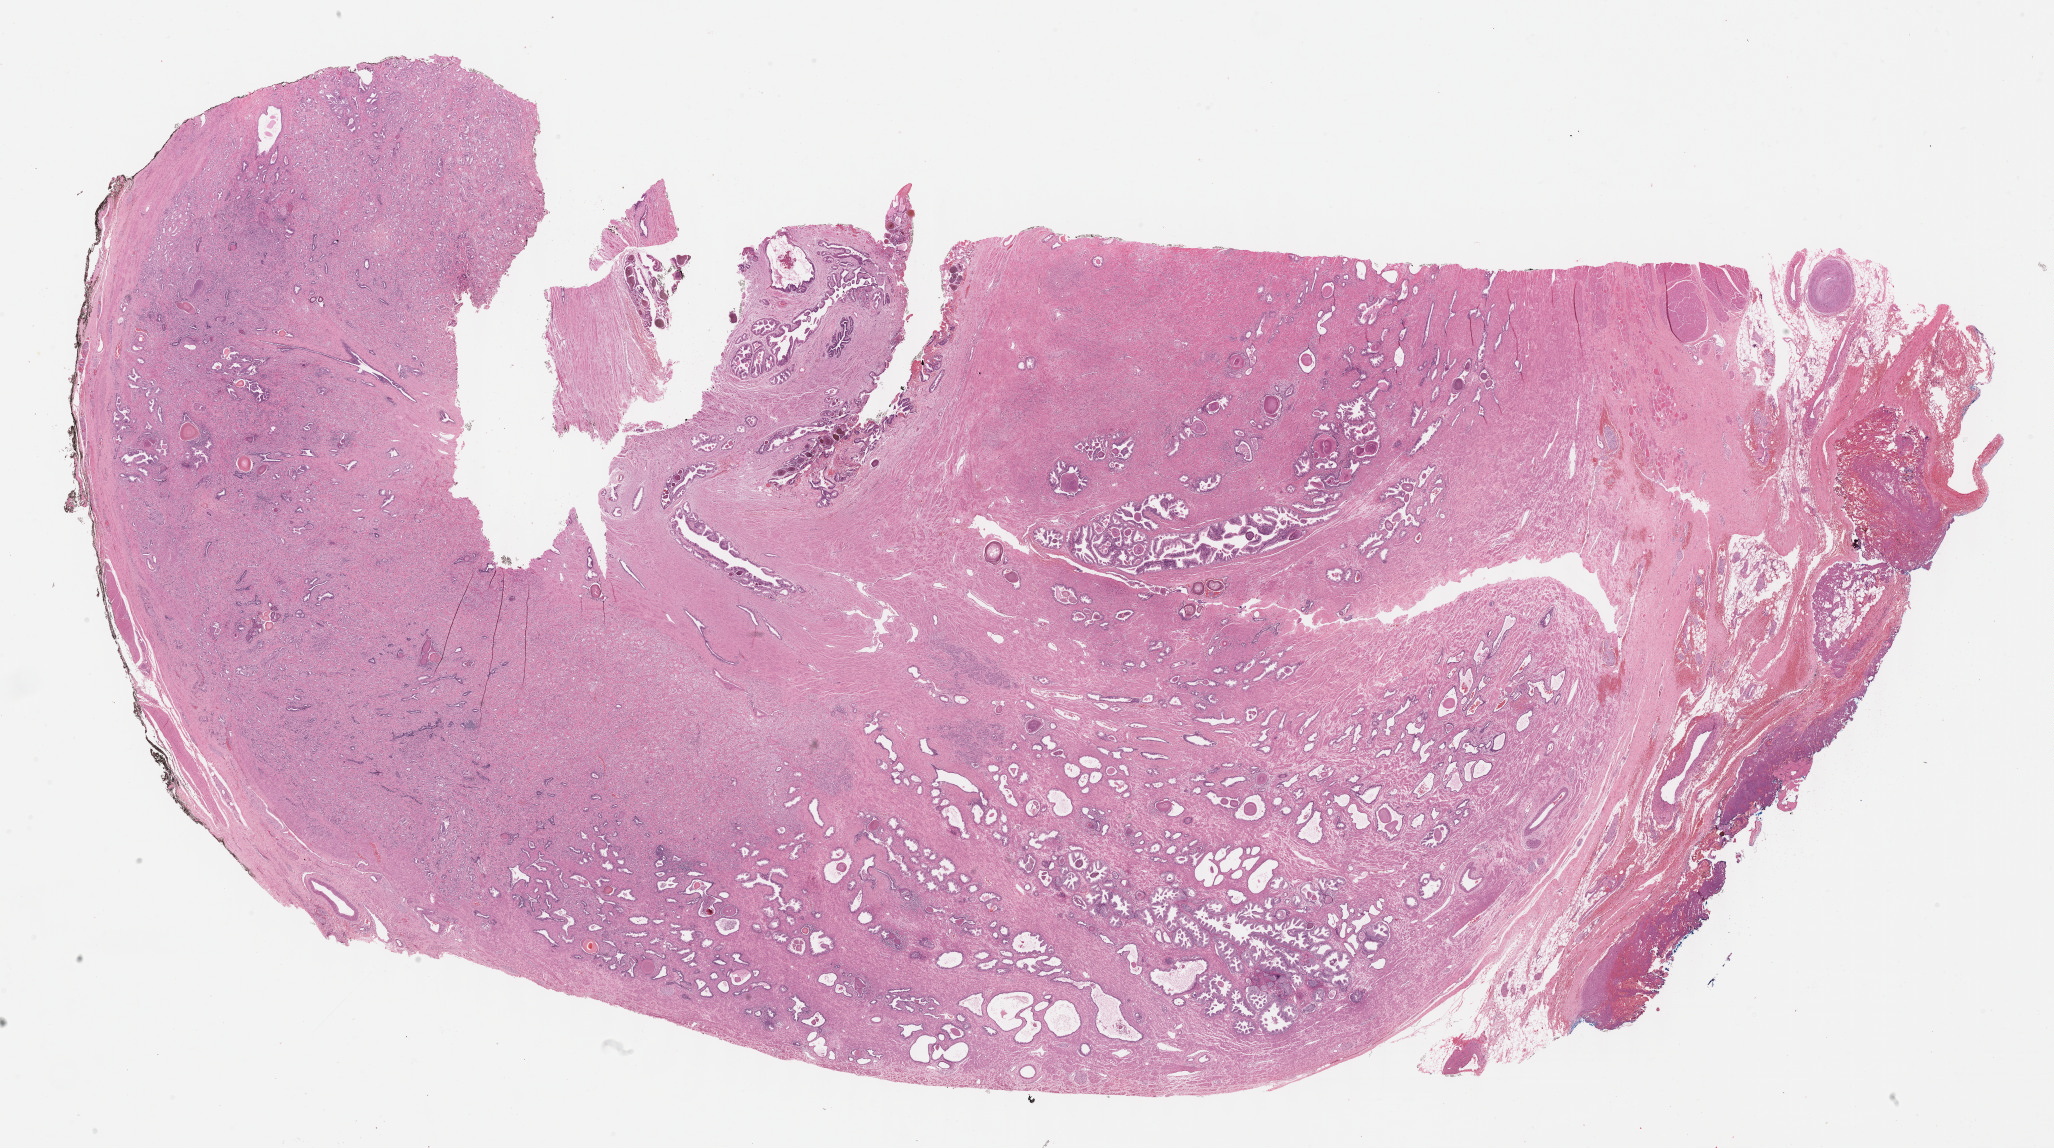
H&E whole-slide image — whole scanned area (about 33.2 x 18.6 mm, from a 40x scan) shown as a low-resolution overview, FFPE section, sample: primary tumour, prostate. Male patient; age at initial diagnosis 67 years. Gleason score: 9 (4+5).
• histologic diagnosis: Adenocarcinoma, NOS (prostate gland)
• lymph nodes positive (case pathology): 0 of 4 examined
• laterality: bilateral